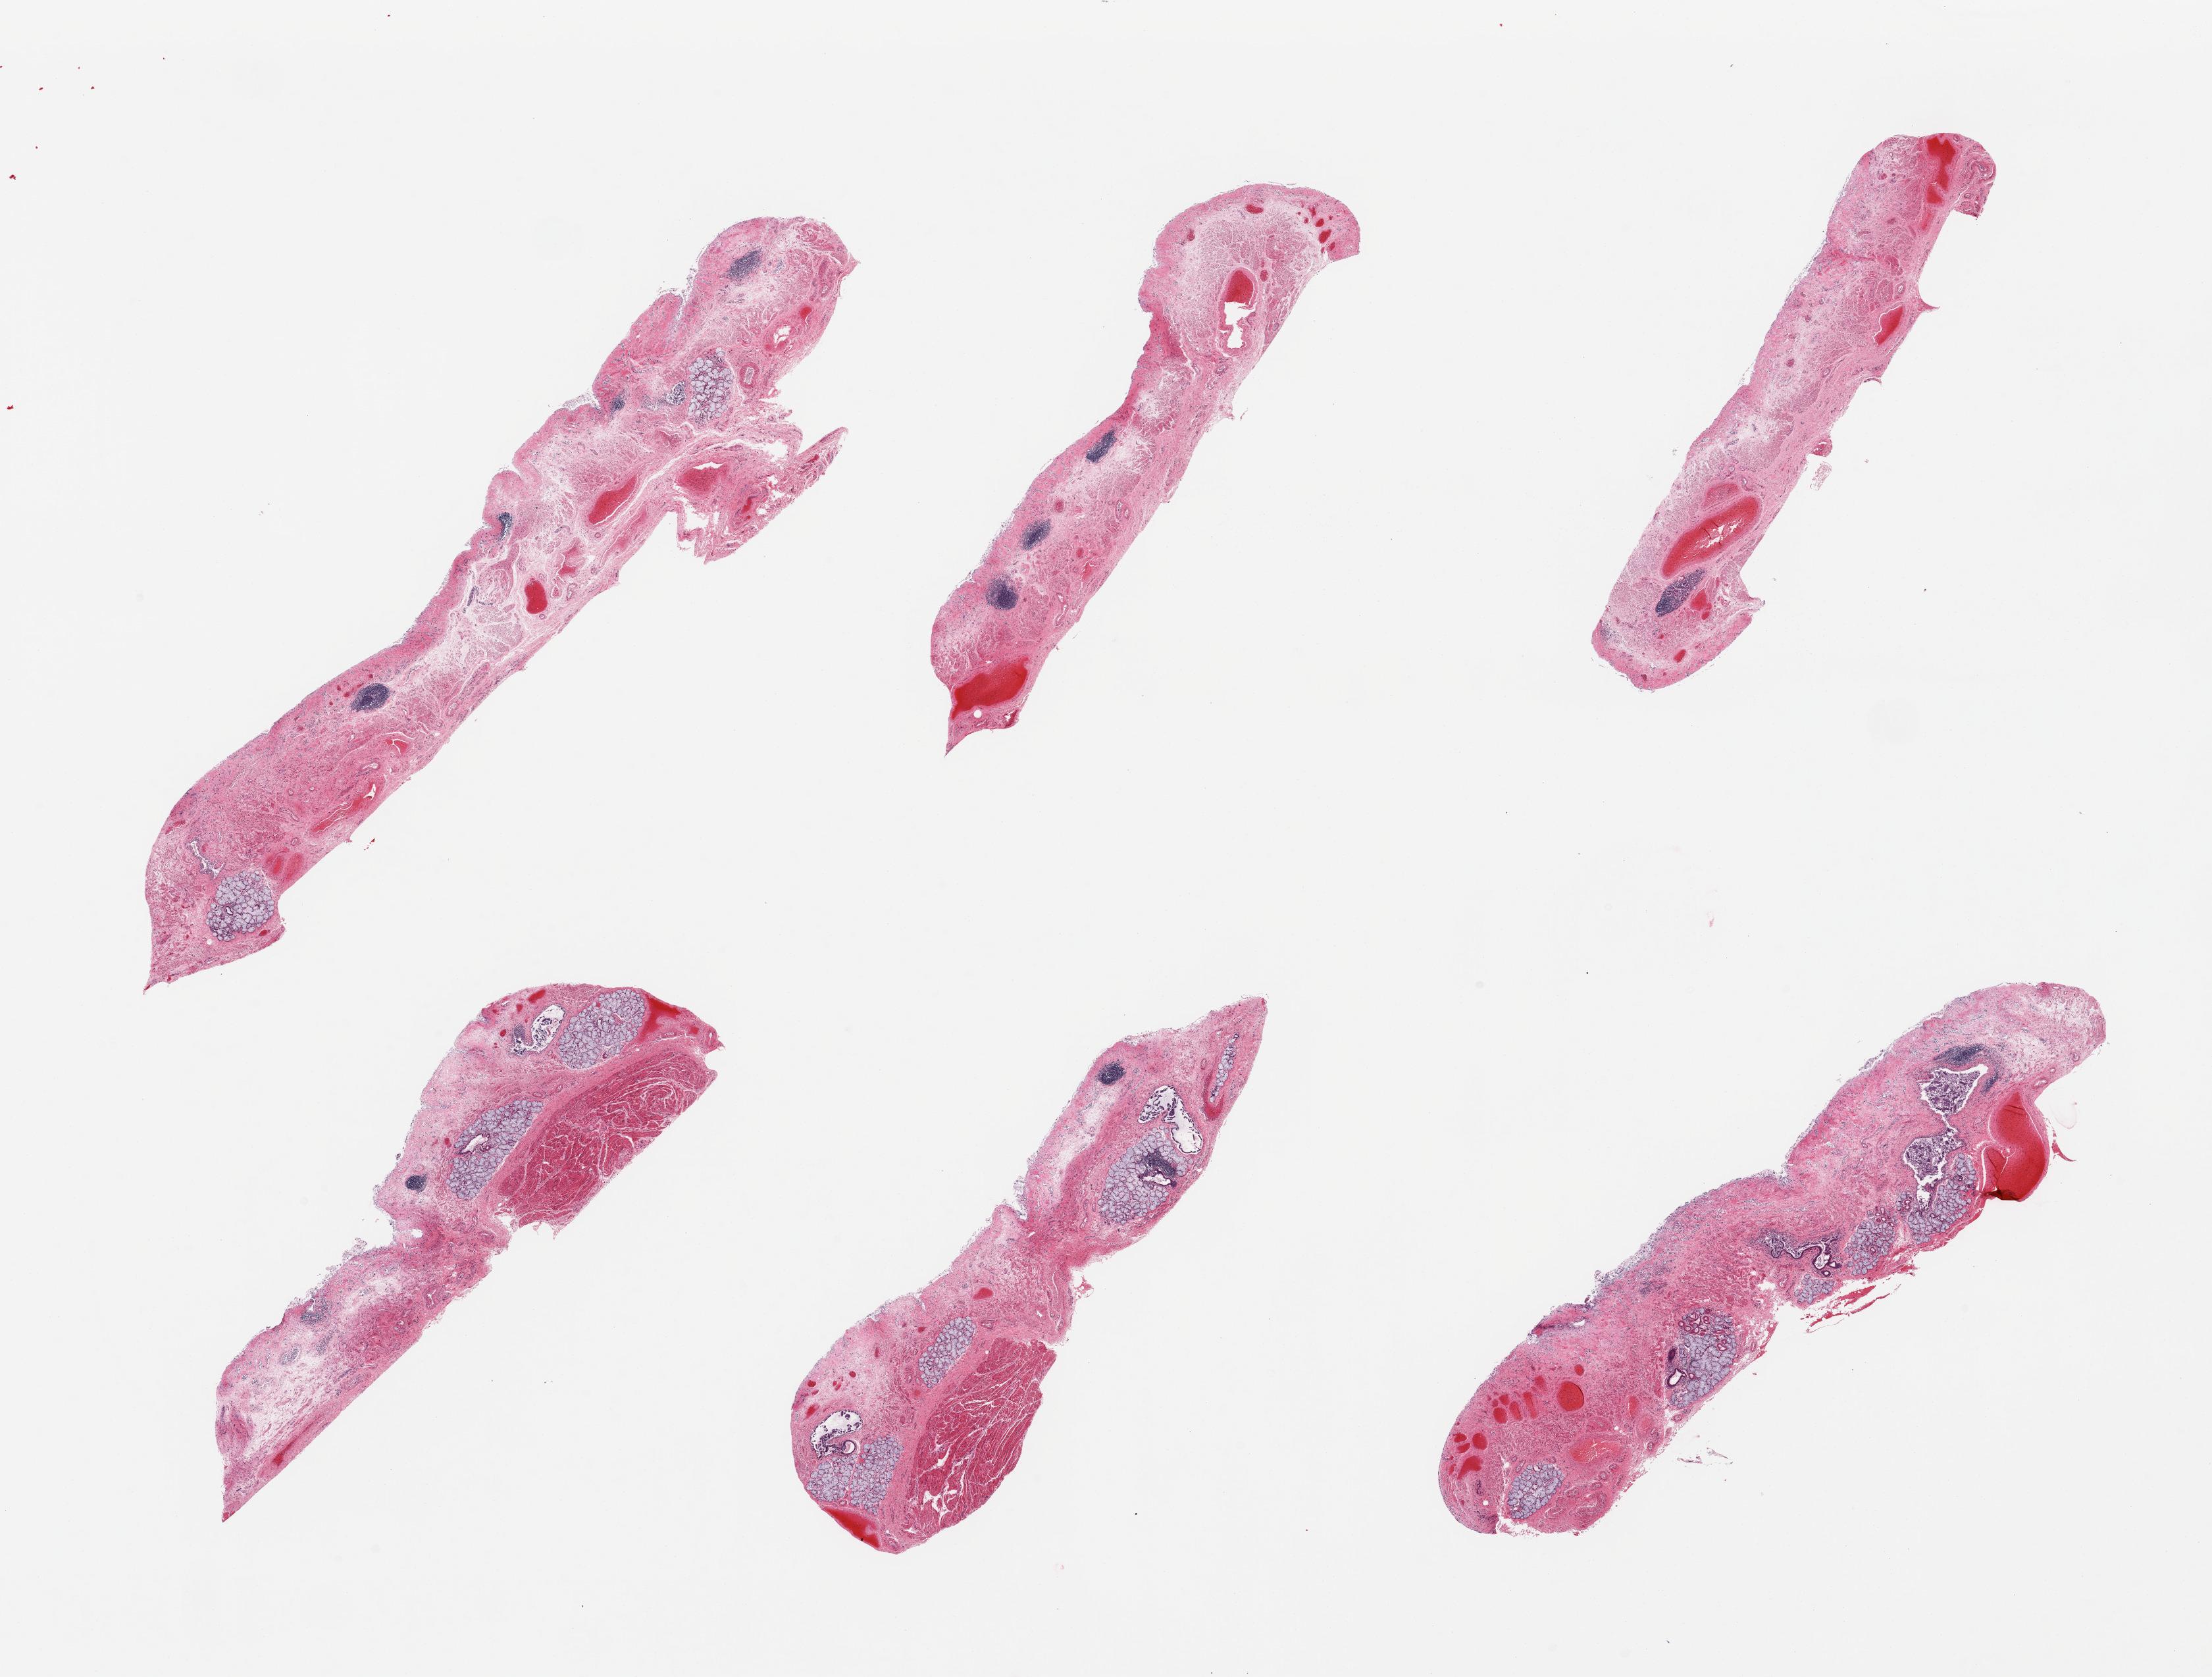
Whole-slide image, H&E stain, a low-resolution overview of the entire scanned area, about 26.6 x 20.2 mm, PAXgene-fixed, paraffin-embedded tissue, target tissue: esophageal mucous membrane, donor tissue sample. Donor sex: male.
Review note (as recorded): 6 pieces, unusually markedly autolyzed; squamous mucosa totally sloughed; submucosal mucus glands prominent.